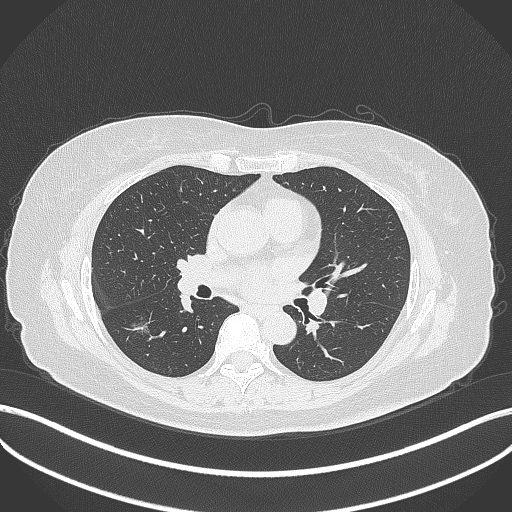
Chest CT, one axial slice. Position 168 of 322 along the scan axis. 120 kVp. Lung window (W 1500 / L -600 HU). 1 mm slice thickness. 512 × 512 image matrix. Female patient, age 64 years. Case-level facts recorded for this patient, not image findings: clinical TNM (as recorded): T1c N0 M0; histopathological grade: G1.
Outlined on this slice (bounding box drawn by a radiologist):
- lung tumour (recorded histology: adenocarcinoma): bounding box <124,311,155,335> (left, top, right, bottom; pixels)